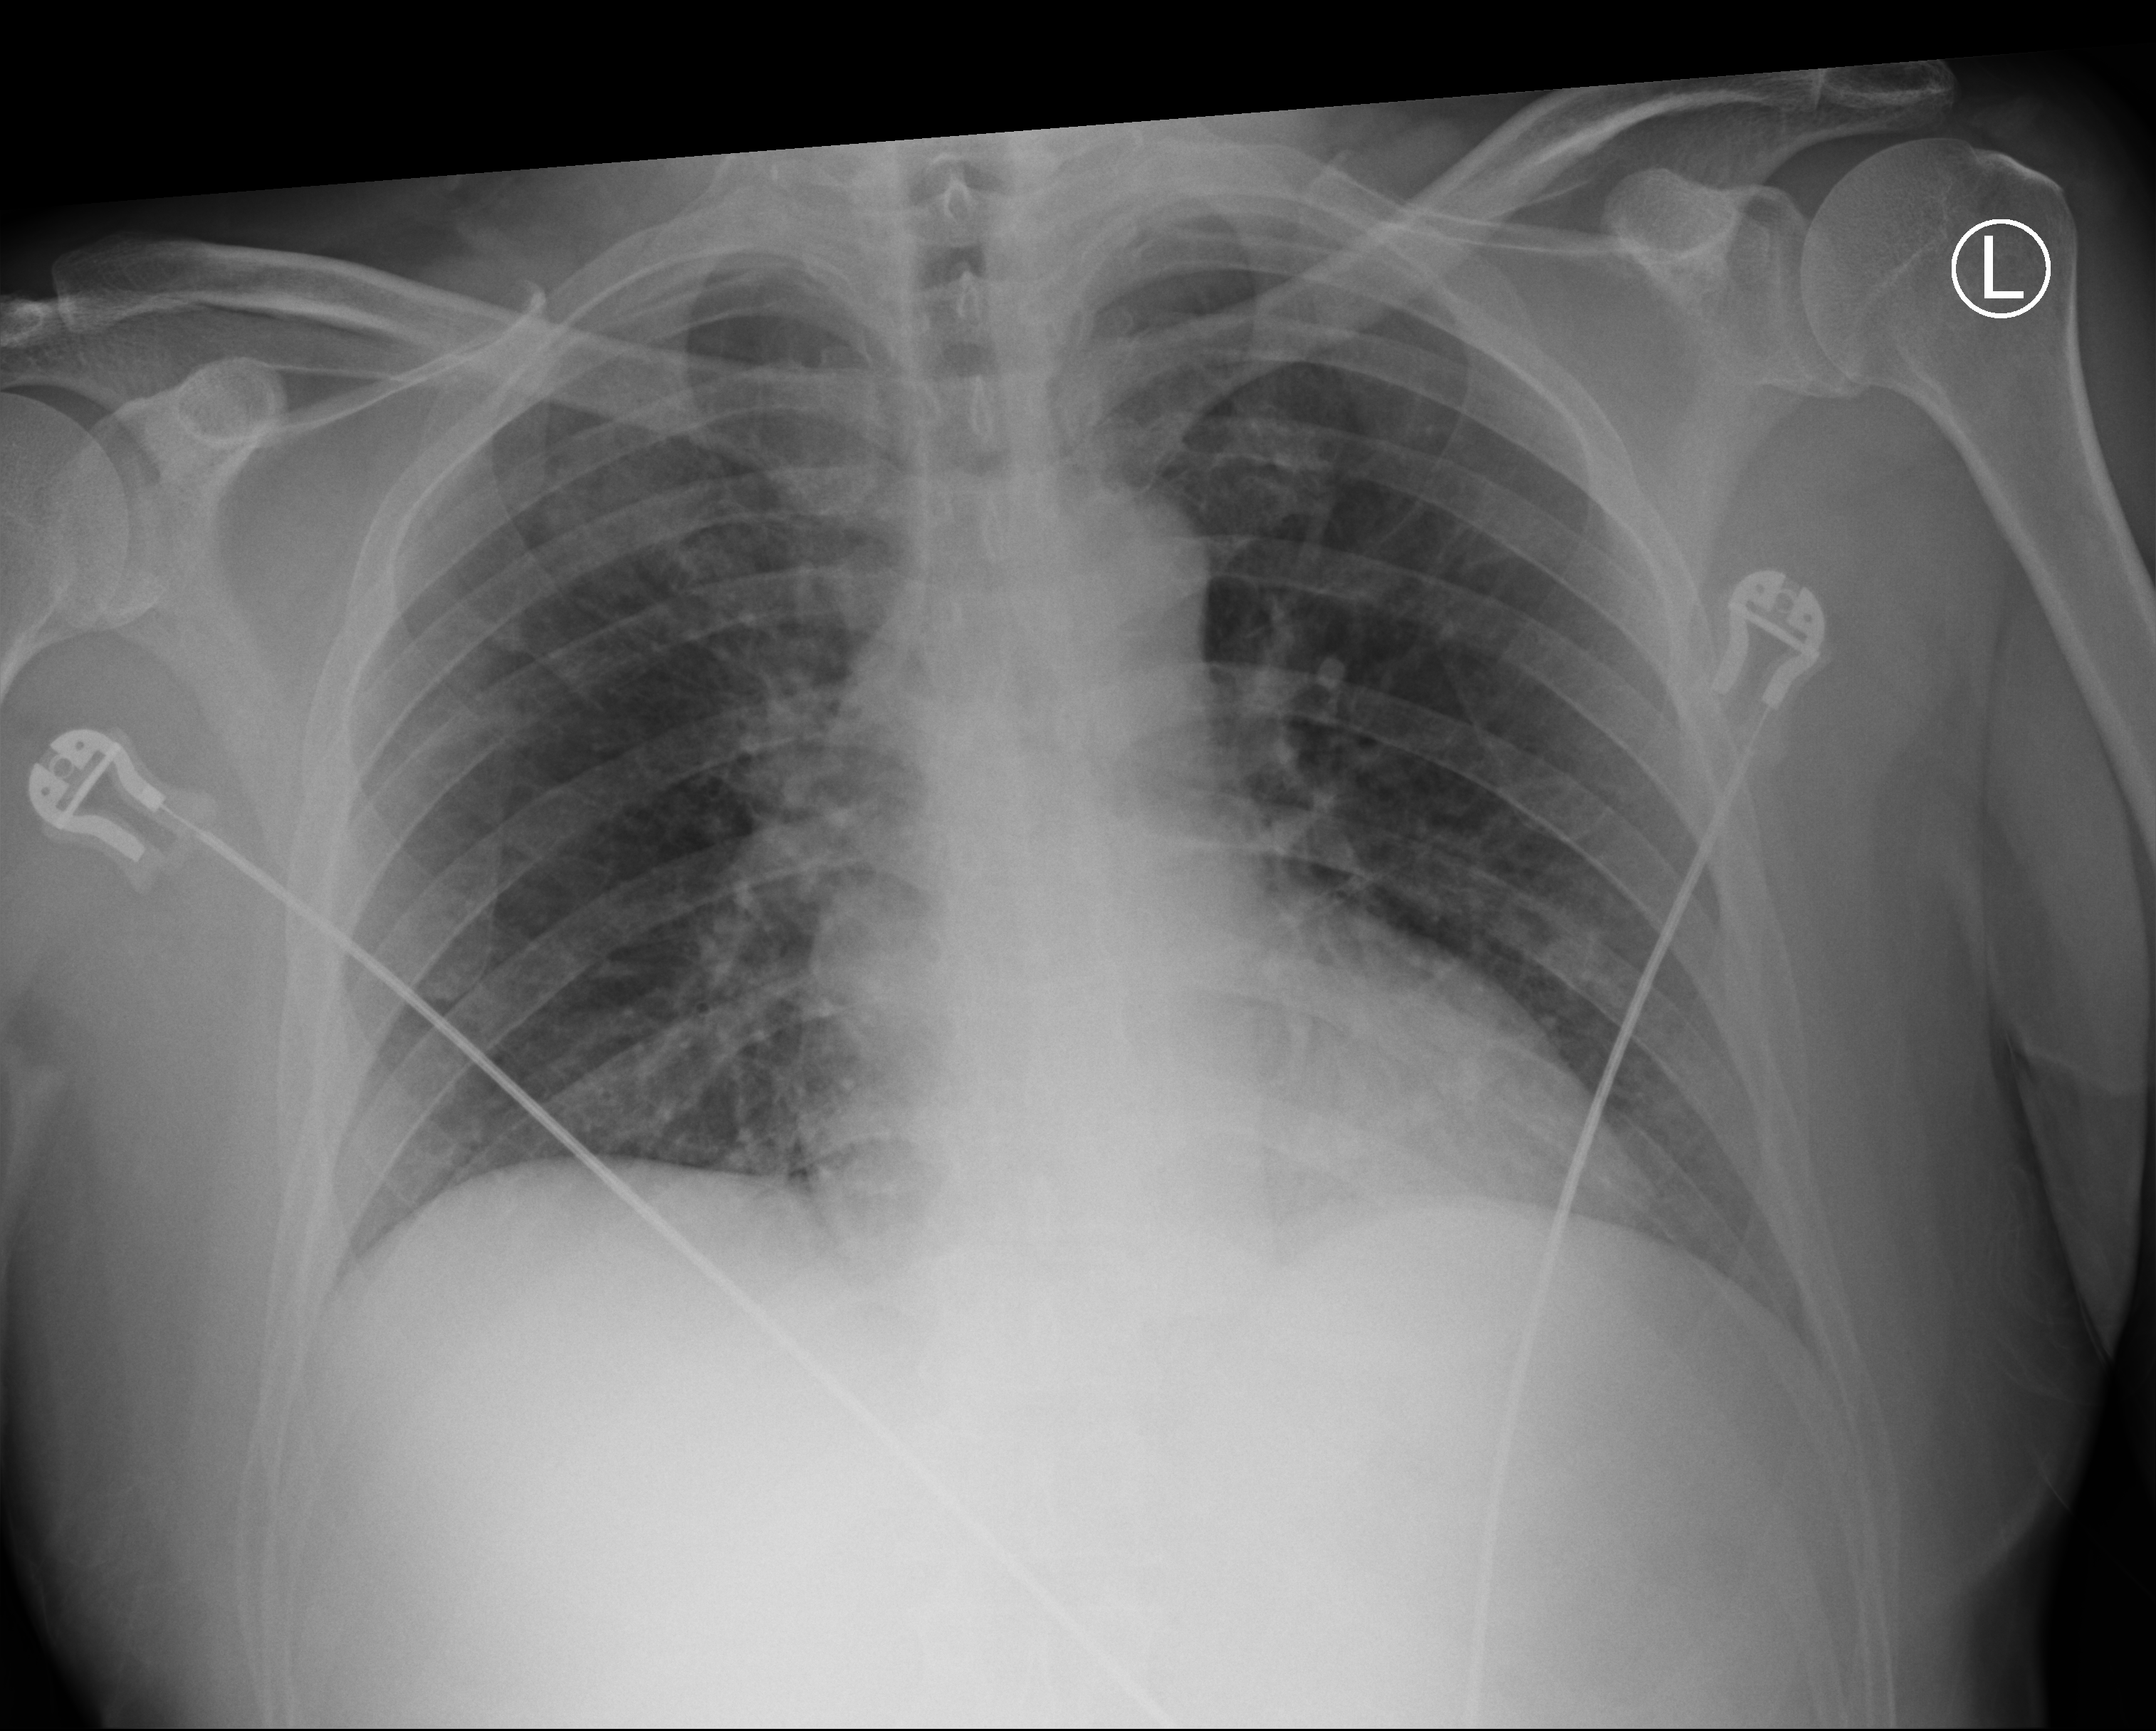
Bedside chest radiograph (computed radiography), anteroposterior (AP) projection. Male patient hospitalised with COVID-19, age 18–59 years.
From the hospital-stay record, not from the radiograph (when in the stay this image was taken is not recorded):
- diabetes (admission record): no
- admitted to intensive care during this hospital stay: no